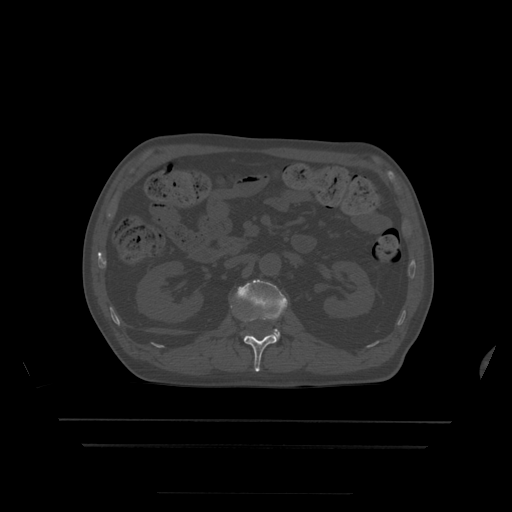
CT including the spine, one axial slice. Position 160 of 522 along the scan axis. Bone window (W 1800 / L 400 HU). 512 × 512 image matrix, field of view 436 × 436 mm. Patient age 68 years. From the clinical record (not read from this slice): primary cancer: urothelial.
Structures marked on this image (semi-automatically segmented with operator editing):
- L1 vertebra: bounding box (x1, y1, x2, y2) in pixels: (231, 306, 277, 372)
- L2 vertebra: (236, 280, 288, 340)